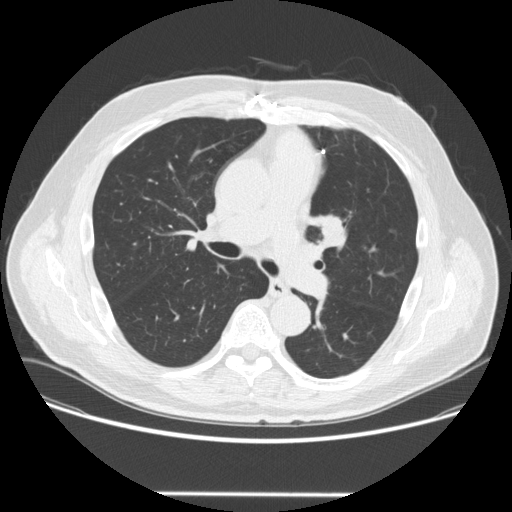
Low-dose screening chest CT, one axial slice; position 160 of 253 along the scan axis; lung window (W 1500 / L -600 HU); 2.5 mm slice thickness; 512 × 512 image matrix.
Annotated regions visible in this slice (outlined manually by an expert reader):
- lesion 1 (tumor, upper lobe of left lung): bounding box (x1, y1, x2, y2) in pixels: (320, 217, 343, 245)